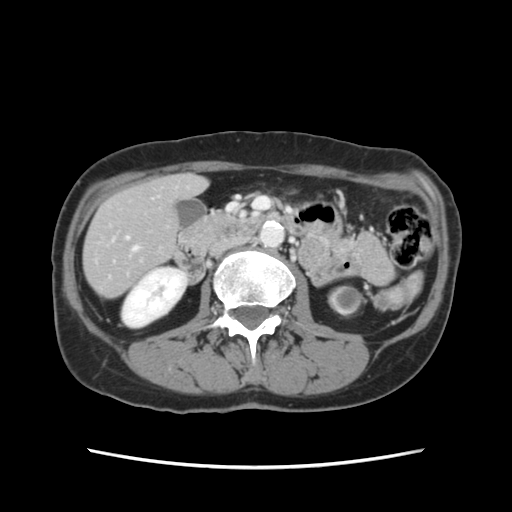
Contrast-enhanced abdominal CT, one axial slice. Slice 39 of 120 in the series (ordered by position). 120 kVp. Soft-tissue window (W 400 / L 40 HU). 512 × 512 image matrix. Female patient, age 70 years. From the clinical record (not read from this slice): diagnosis: colorectal cancer liver metastases, imaged before liver resection; multiple liver metastases: no; largest metastasis: 2.5 cm; disease in both lobes: no.
Structures marked on this image (manually delineated by an expert):
- hepatic veins: box from (x=133, y=247) to (x=138, y=251) px
- liver: (x=84, y=176)–(x=205, y=297)
- planned liver remnant (the part of the liver to remain after resection): (x=84, y=175)–(x=205, y=297)
- portal vein (with intrahepatic branches): (x=126, y=236)–(x=129, y=239)